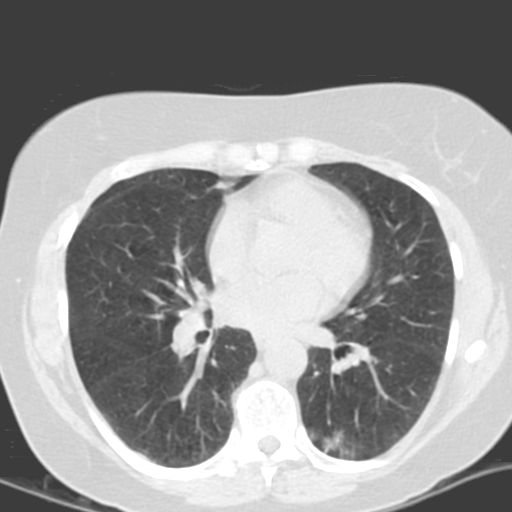
Low-dose screening chest CT, axial slice; second annual screen; lung window (W 1500 / L -600 HU); 3.2 mm slice thickness; slice 76 of 161 in the series. Female, age 55 years at enrolment. Current smoker at enrolment.
Lesion marked by an expert reader, bounding box <305,411,378,466> (left, top, right, bottom; pixels). The screening reader recorded 4 non-calcified nodules or masses ≥4 mm on this exam (left lower lobe, left lower lobe, left upper lobe, right middle lobe); which of them this box marks is not recorded. Lung cancer was diagnosed 688 days after this screen (after the third annual screen): adenocarcinoma with mixed subtypes, left lower lobe, poorly differentiated (G3), stage IA (AJCC 6th edition), 21 mm at pathology.